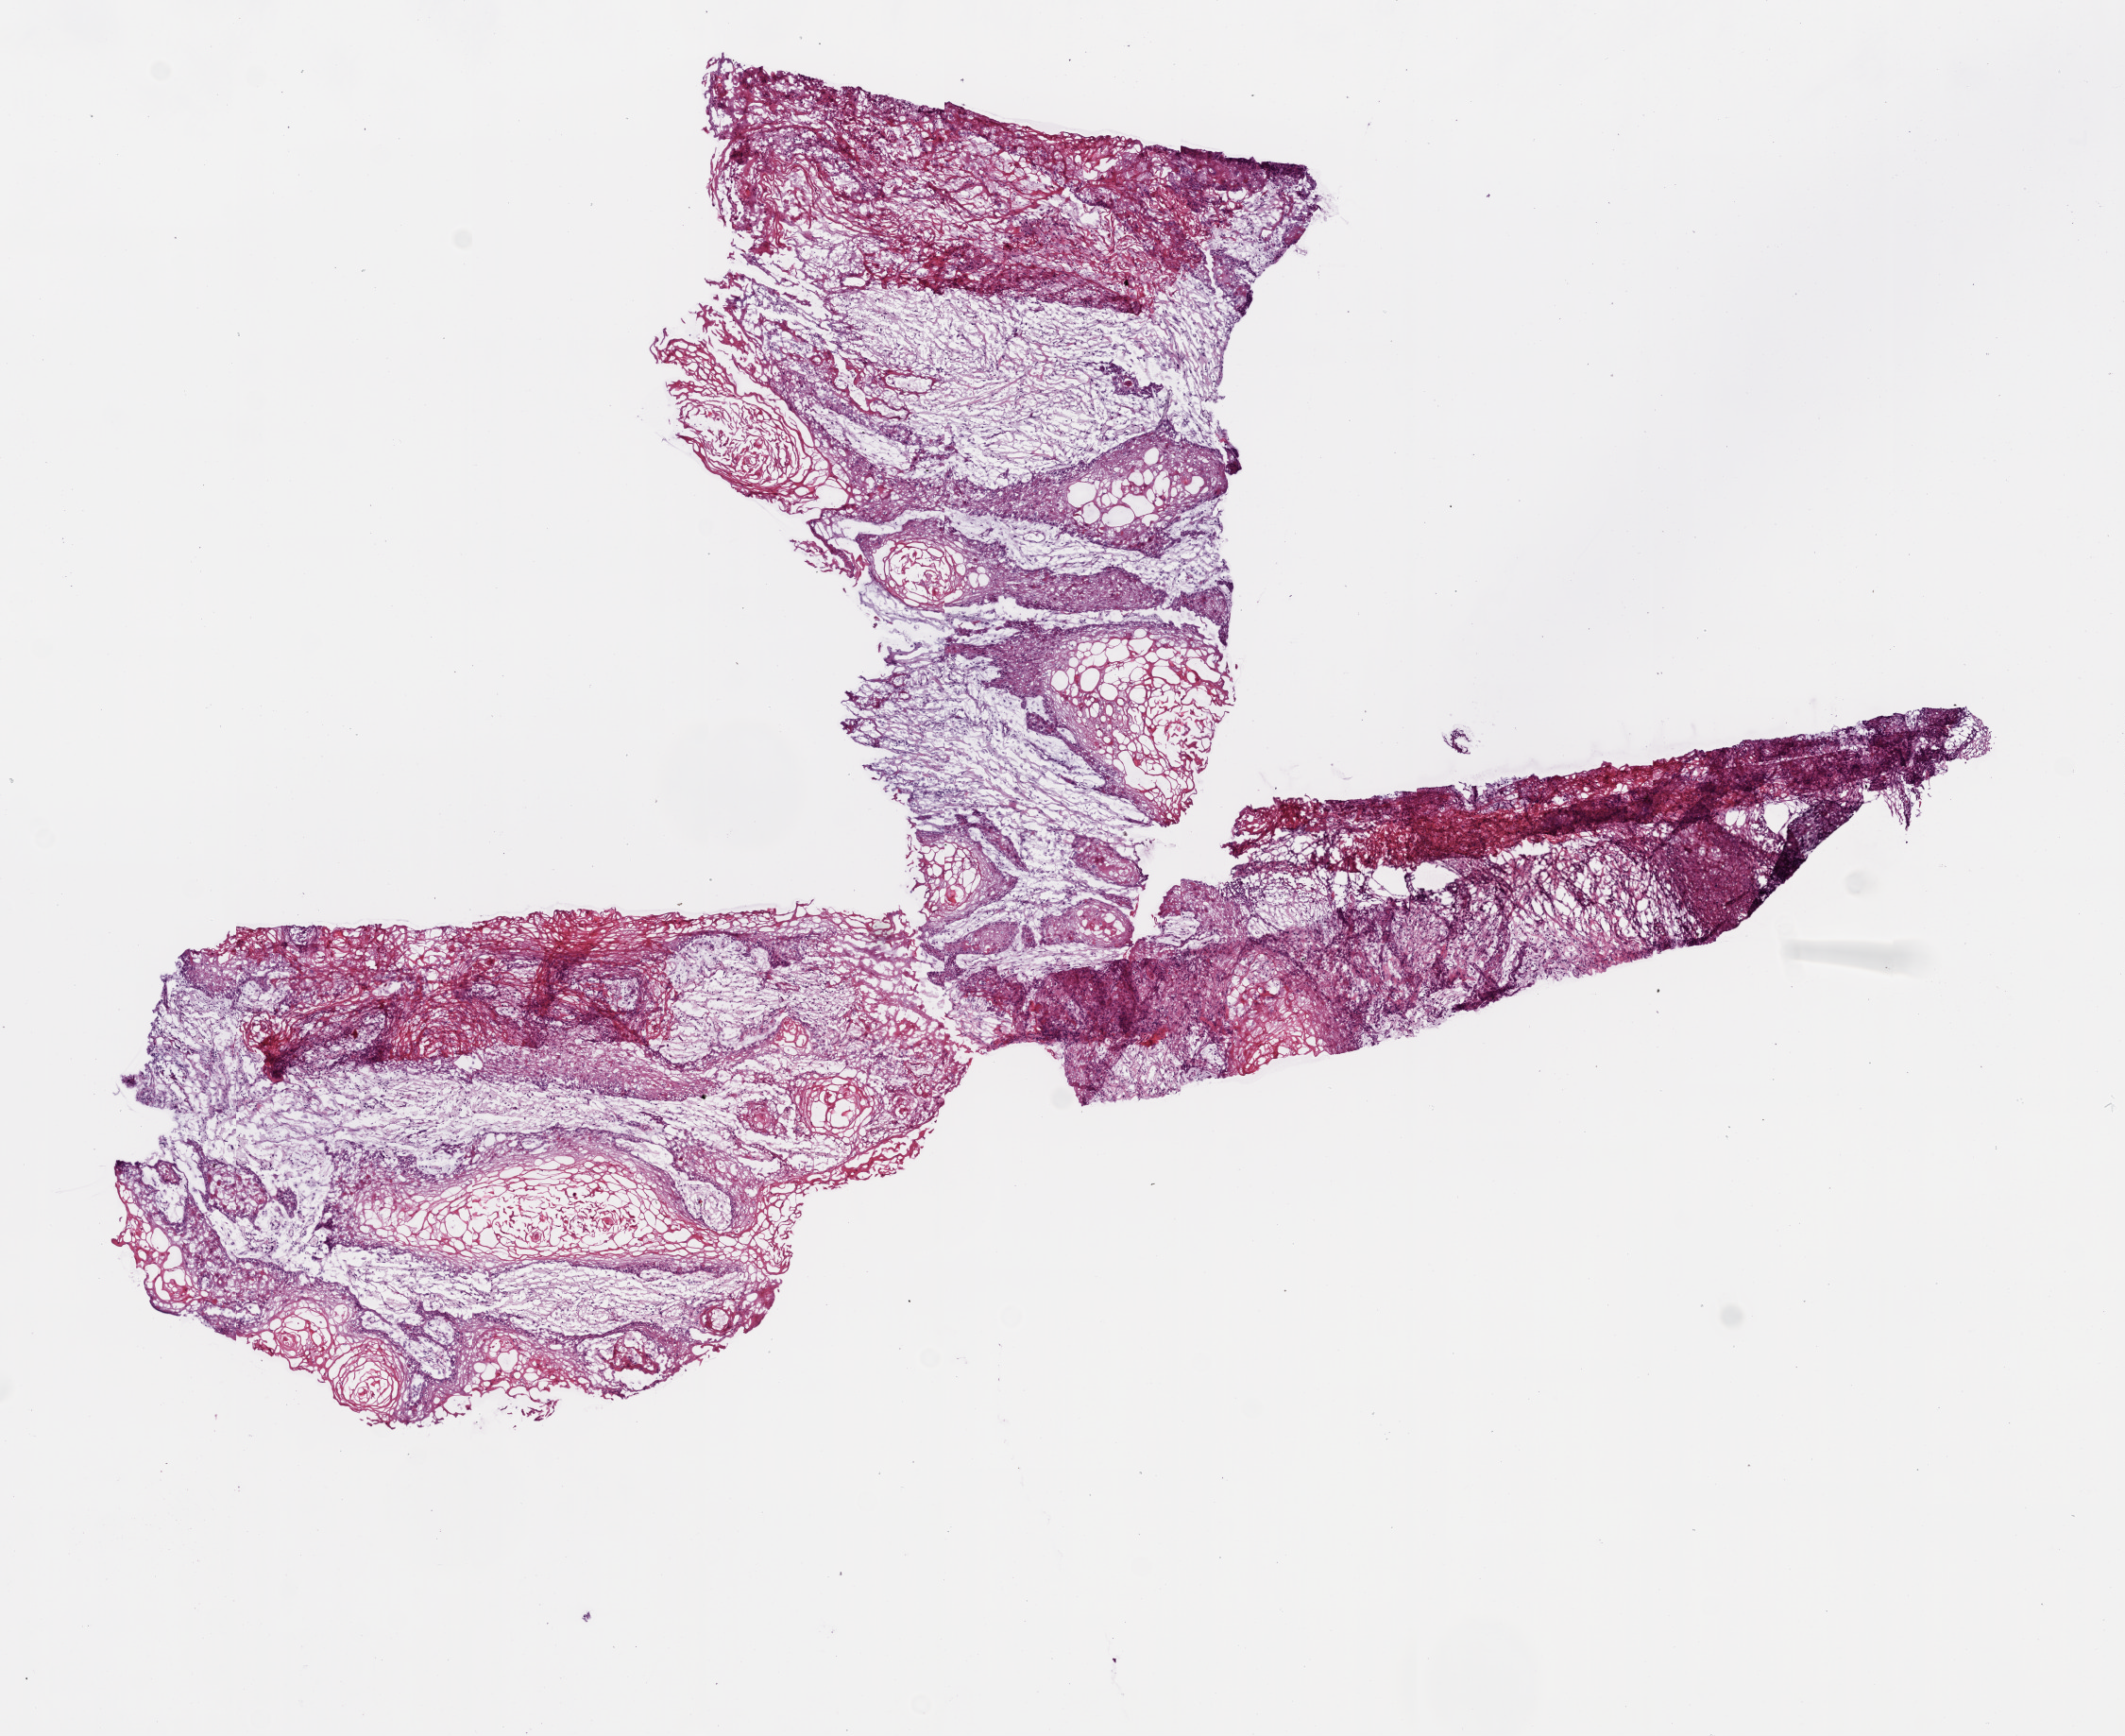
Digitized H&E-stained tissue section (whole slide) — low-resolution overview of the scanned area, about 9.0 x 7.4 mm (slide scanned at 20x); frozen section; head and neck, primary tumour sample. Male, age 68 years at initial diagnosis. Histologic grade: G2 (moderately differentiated). Pathologist review of this section (percent, as recorded): tumour cells 70%, tumour nuclei 85%, normal cells 0%, stromal cells 30%, necrosis 0%.
AJCC pathologic stage: IVA (7th edition). Histologic diagnosis: Squamous cell carcinoma, NOS (cheek mucosa). Lymph nodes positive (case pathology): 6 of 14 examined.